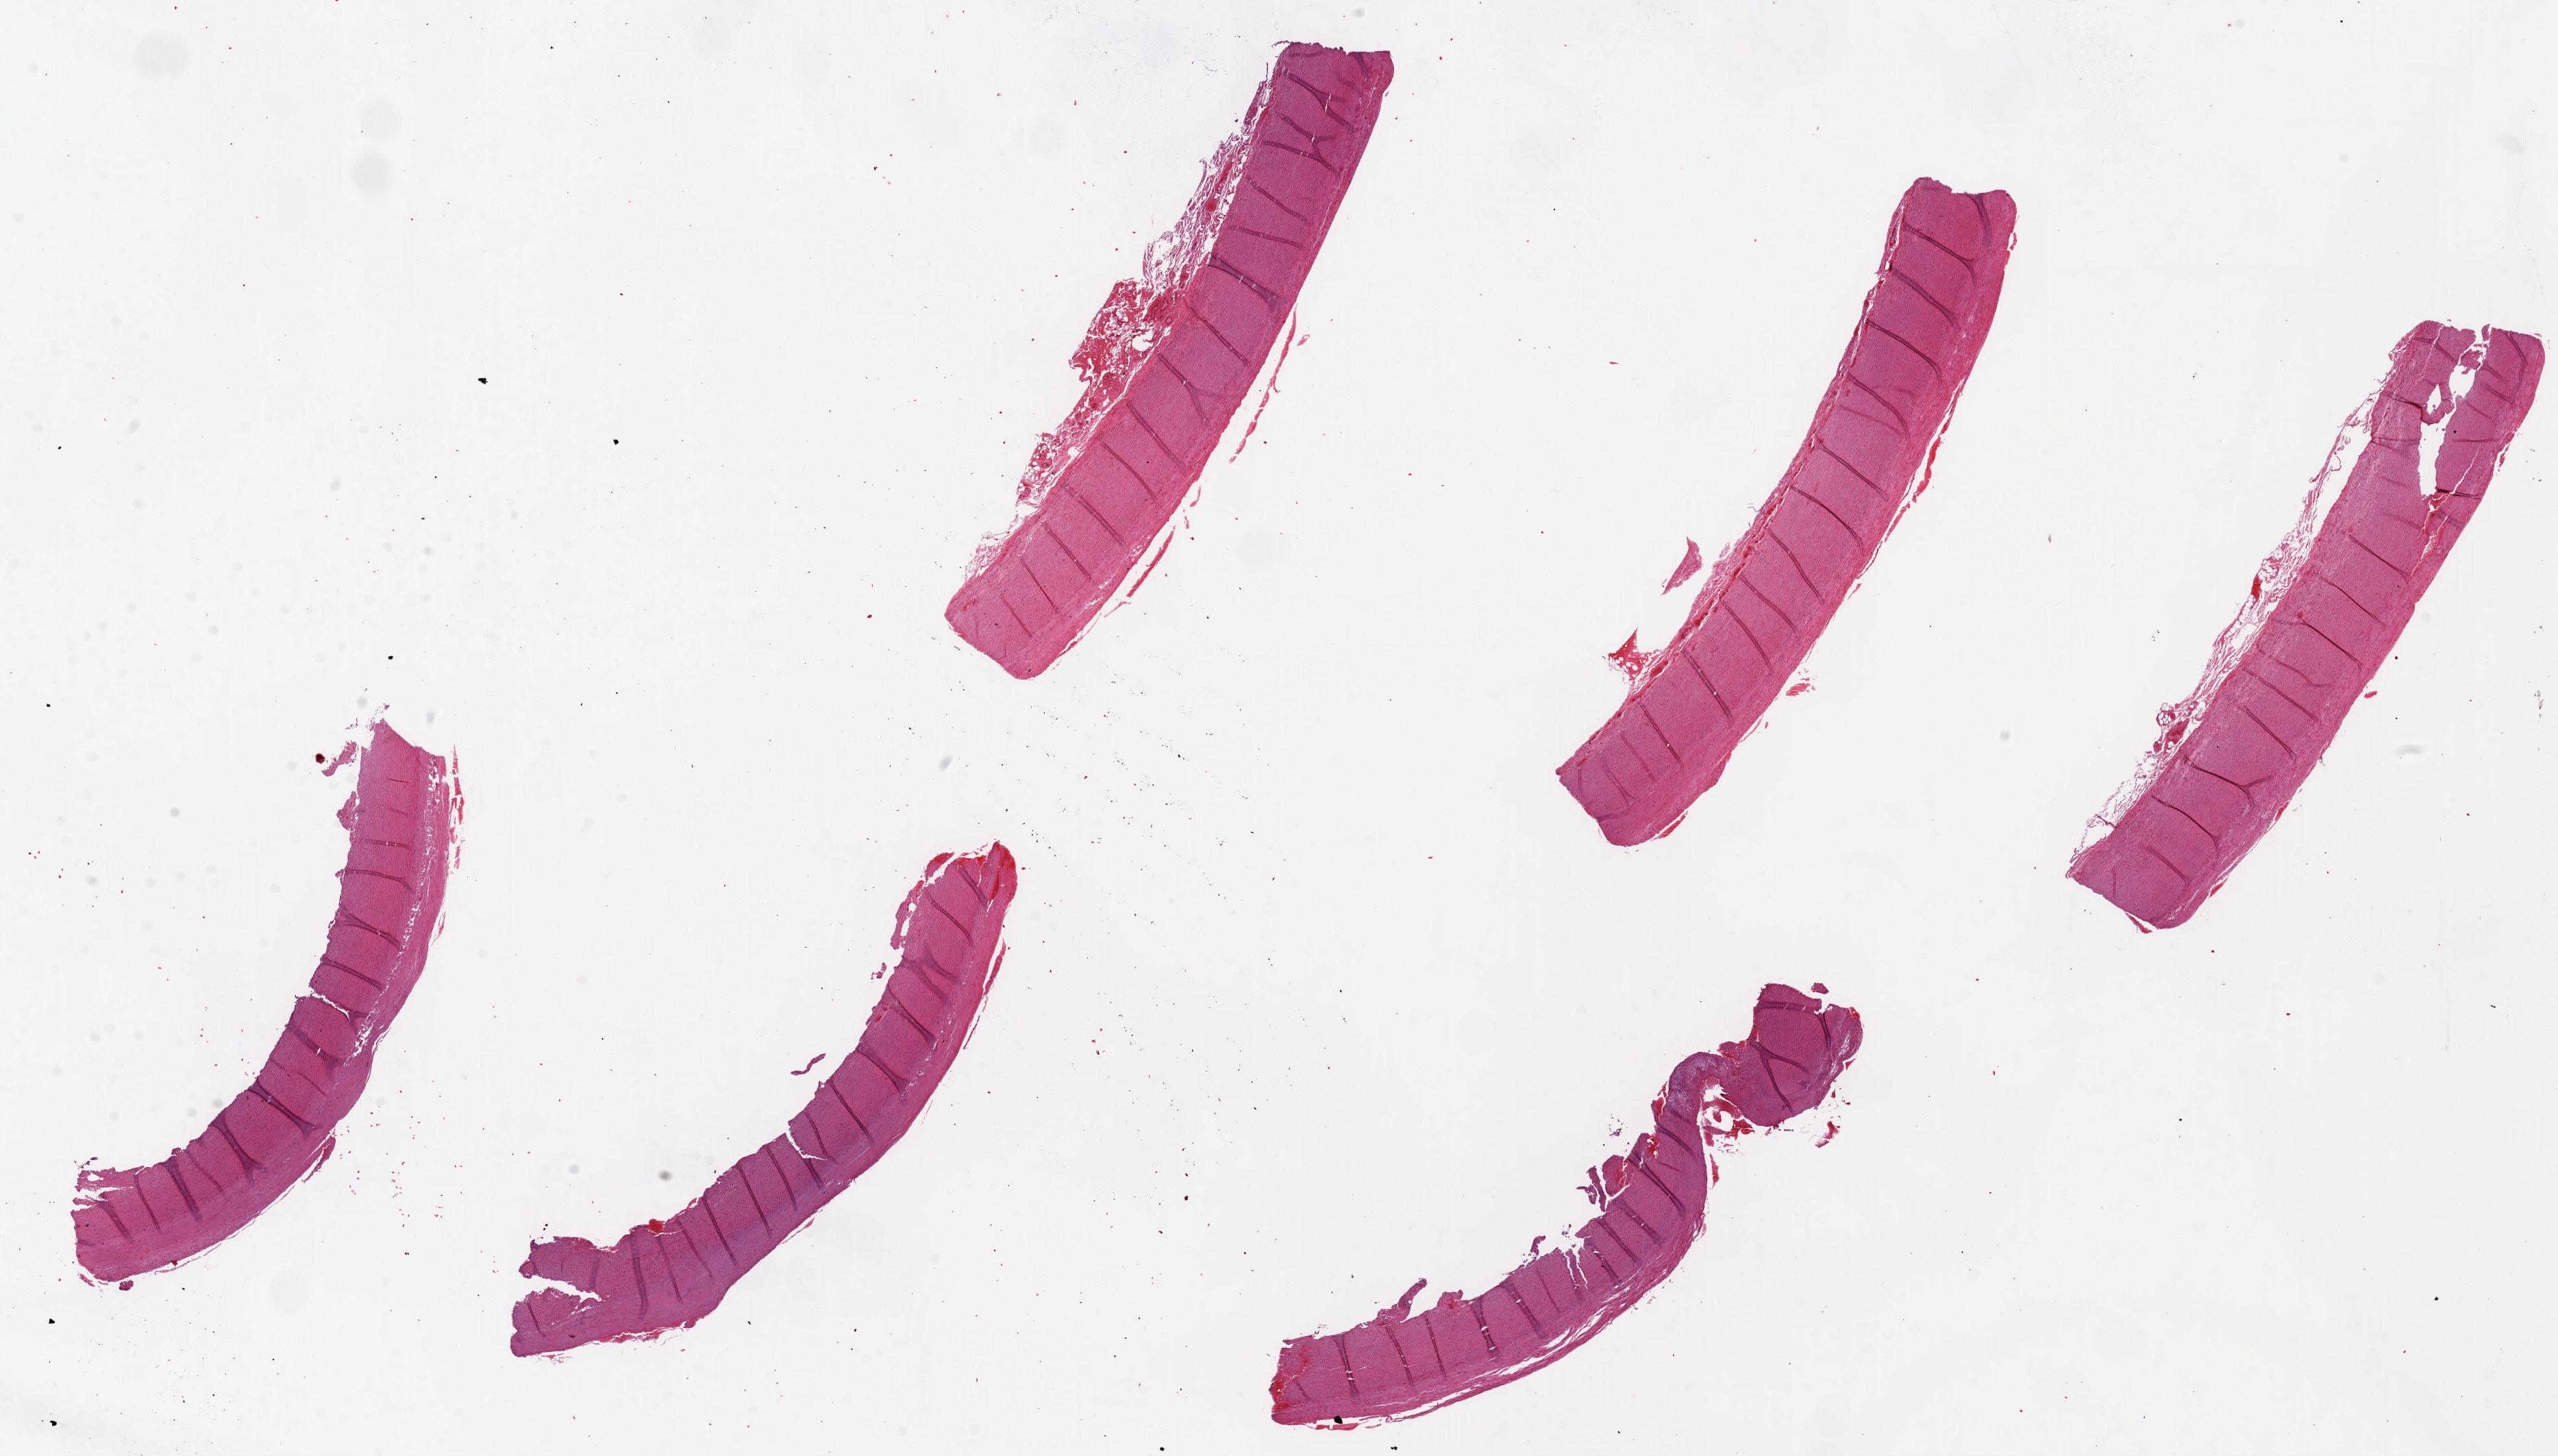
Haematoxylin and eosin whole-slide image — shown as a low-resolution overview of the whole scanned area (about 29.5 x 16.8 mm). PAXgene-fixed paraffin-embedded (PFPE) section. Section of aorta (target tissue). Tissue donor sample. Male donor.
Review note (as recorded): 6 pieces ~8x1mm.